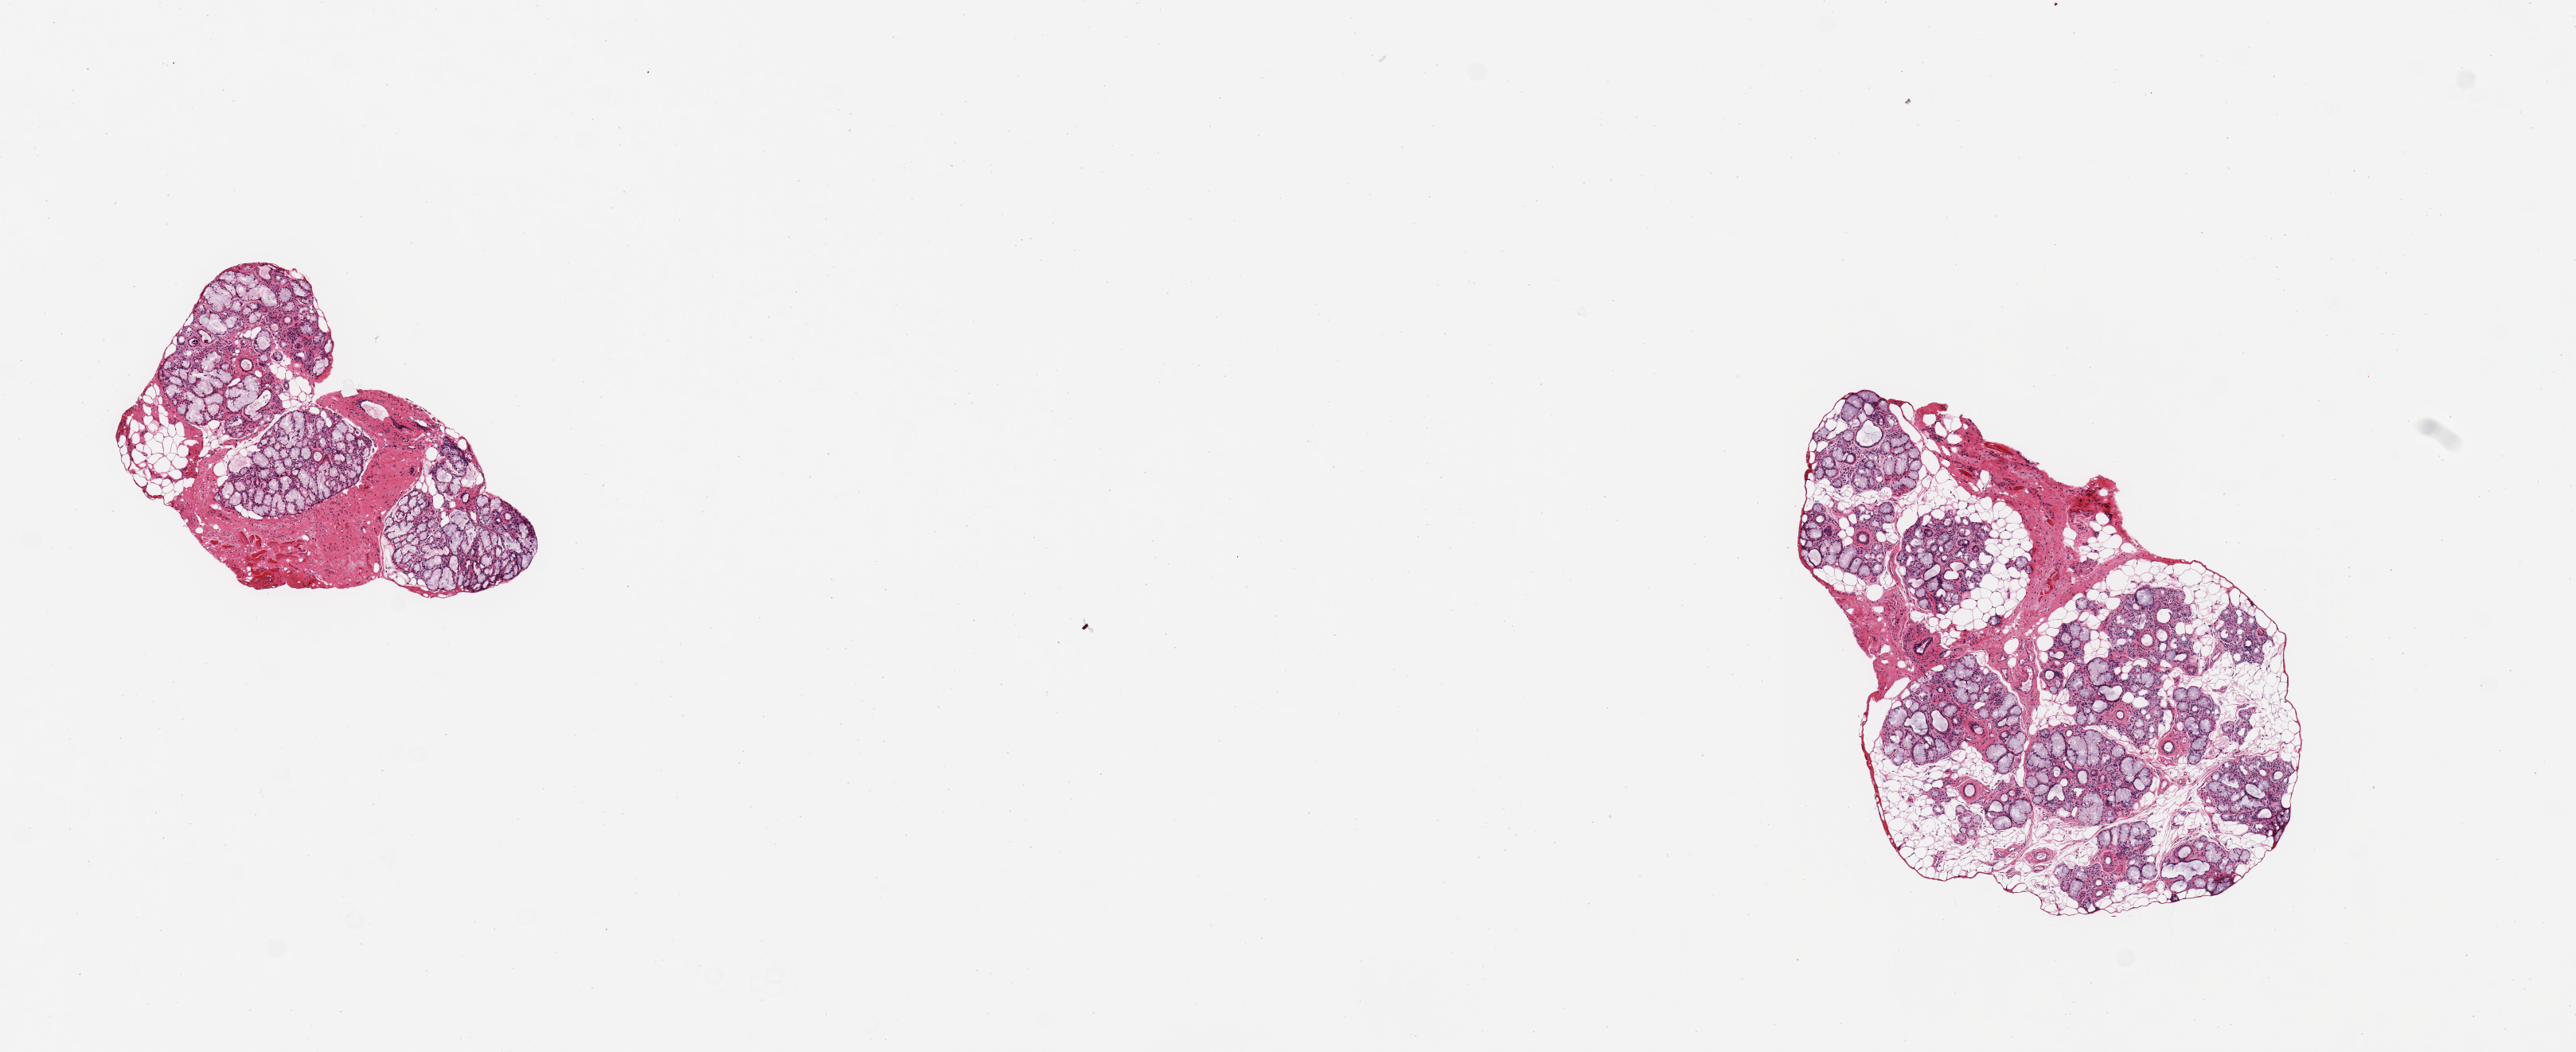
Hematoxylin and eosin (H&E) whole-slide image, whole scanned area (about 12.8 x 5.2 mm) shown as a low-resolution overview; PAXgene-fixed paraffin-embedded (PFPE) section; sampled site (target tissue): minor salivary gland; donor tissue sample. Donor: male.
Reviewer comment on this tissue sample: 6 pieces, target mucosa up to ~0.3mm, complete mucosal glandular autolysis/sloughing.